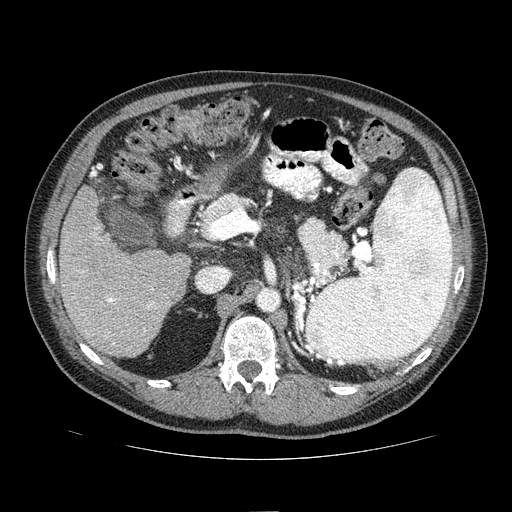
Contrast-enhanced abdominal CT (liver protocol), one axial slice; slice 32 of 81 in the series (ordered by position); reconstruction kernel STANDARD; 100 kVp; one of 2 acquisitions stored at this slice position; soft-tissue window (W 400 / L 40 HU); 512 × 512 image matrix. Case-level facts recorded for this patient, not image findings: diagnosis: hepatocellular carcinoma (patient treated with transarterial chemoembolisation; whether this scan precedes or follows treatment is not stated here); TNM stage (as recorded): Stage-IIIA; Child-Pugh class: A; tumour differentiation: well differentiated; tumour nodularity: multinodular.
Annotated regions visible in this slice (semi-automatically segmented with operator editing):
- liver parenchyma outside the tumour (the mass and vessels are separate outlines, so this box may not span the whole liver): bounding box <58,186,190,356> (left, top, right, bottom; pixels)
- liver vessels: <77,227,154,345>